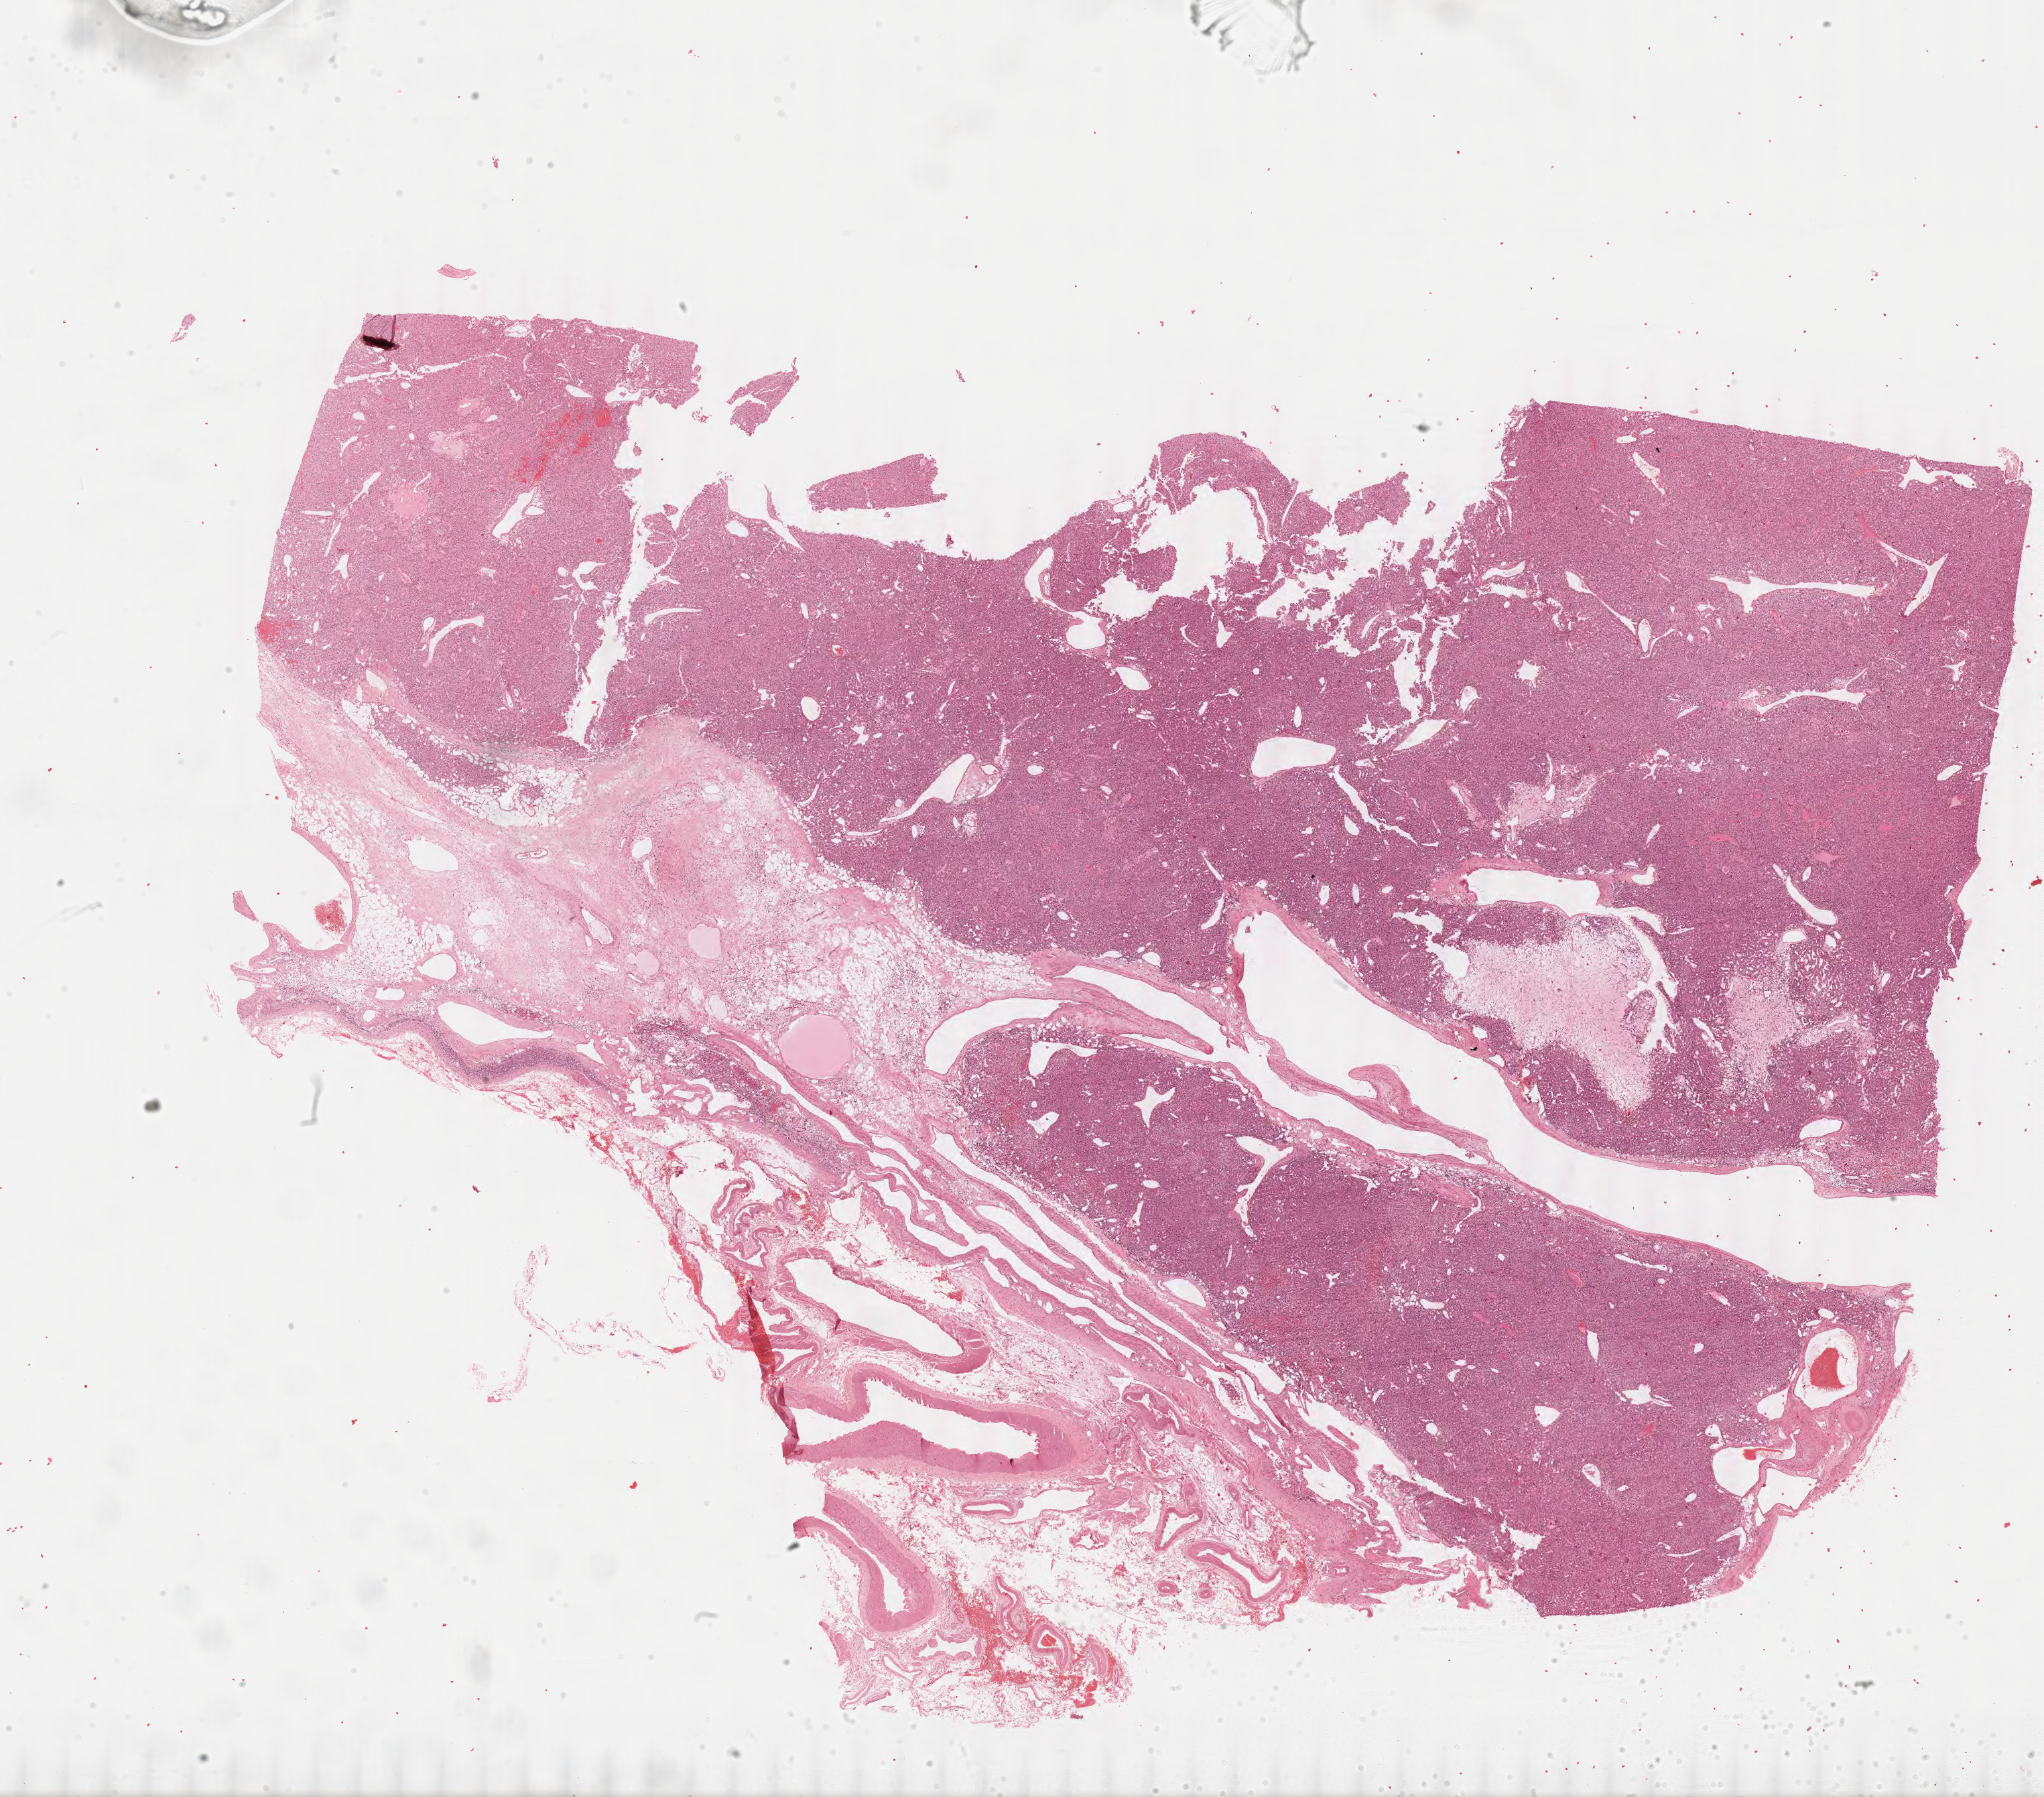
H&E-stained whole-slide image, shown as a low-resolution overview of the whole scanned area (about 24.1 x 21.2 mm); formalin-fixed paraffin-embedded (FFPE) diagnostic section; adrenal cortex, primary tumour sample. Female, age 27 years at initial diagnosis.
Histologic diagnosis: Adrenal cortical carcinoma.